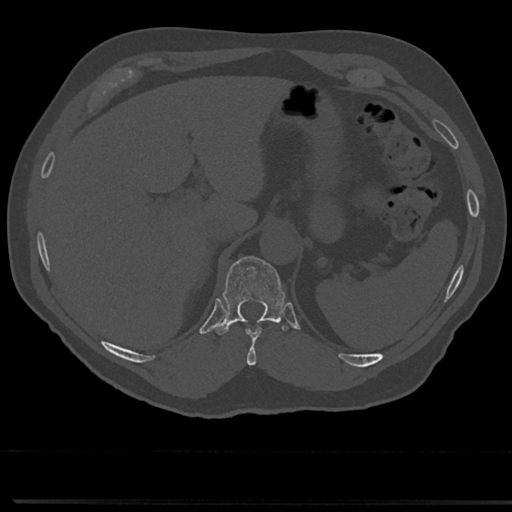
CT including the spine, one axial slice; position 221 of 817 along the scan axis; reconstruction kernel Br40s/3; bone window (W 1800 / L 400 HU); 512 × 512 image matrix. Patient: male, 61 years. Case-level facts recorded for this patient, not image findings: primary cancer: prostate.
Annotated regions visible in this slice (semi-automatic segmentation, software-assisted and operator-edited):
- T10 vertebra: bounding box <244,320,275,366> (left, top, right, bottom; pixels)
- T11 vertebra: <219,256,284,333>